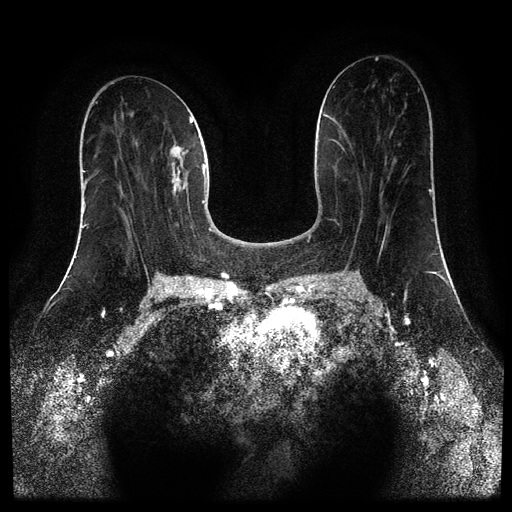
Breast MRI (dynamic contrast-enhanced, multi-phase), one axial slice; position 43 of 110 along the scan axis; dynamic contrast-enhanced series, time point 2 of 5 at this slice position (early post-contrast); 1.5 T; TE 2.6 ms, TR 5.4 ms; 2 mm slice thickness; 512 × 512 image matrix, field of view 340 × 340 mm. Female patient, age 43 years.
Annotated regions visible in this slice (semi-automatic segmentation, software-assisted and operator-edited):
- breast lesion (labelled 'tumour' in the annotation; benign lesions carry a separate 'benign' label): bounding box (x1, y1, x2, y2) in pixels: (170, 146, 188, 196)